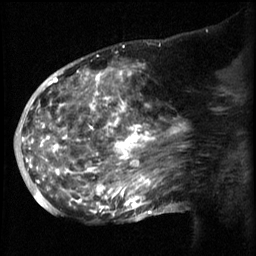
Breast MRI (dynamic contrast-enhanced), one sagittal slice. 3 images stored at this slice position (order not interpretable as contrast timing). 1.5 T. TE 4.2 ms, TR 8.2 ms. 2.3 mm slice thickness. 256 × 256 image matrix. Female patient, age 50 years.
Outlined on this slice (semi-automatically segmented with operator editing):
- analysis volume of interest (the breast-tissue region the enhancement analysis was run in; not a lesion): box from (x=50, y=64) to (x=169, y=217) px
- tumour enhancement mask (voxels above the 70 % enhancement threshold inside the analysis volume of interest): (x=50, y=64)–(x=161, y=217)